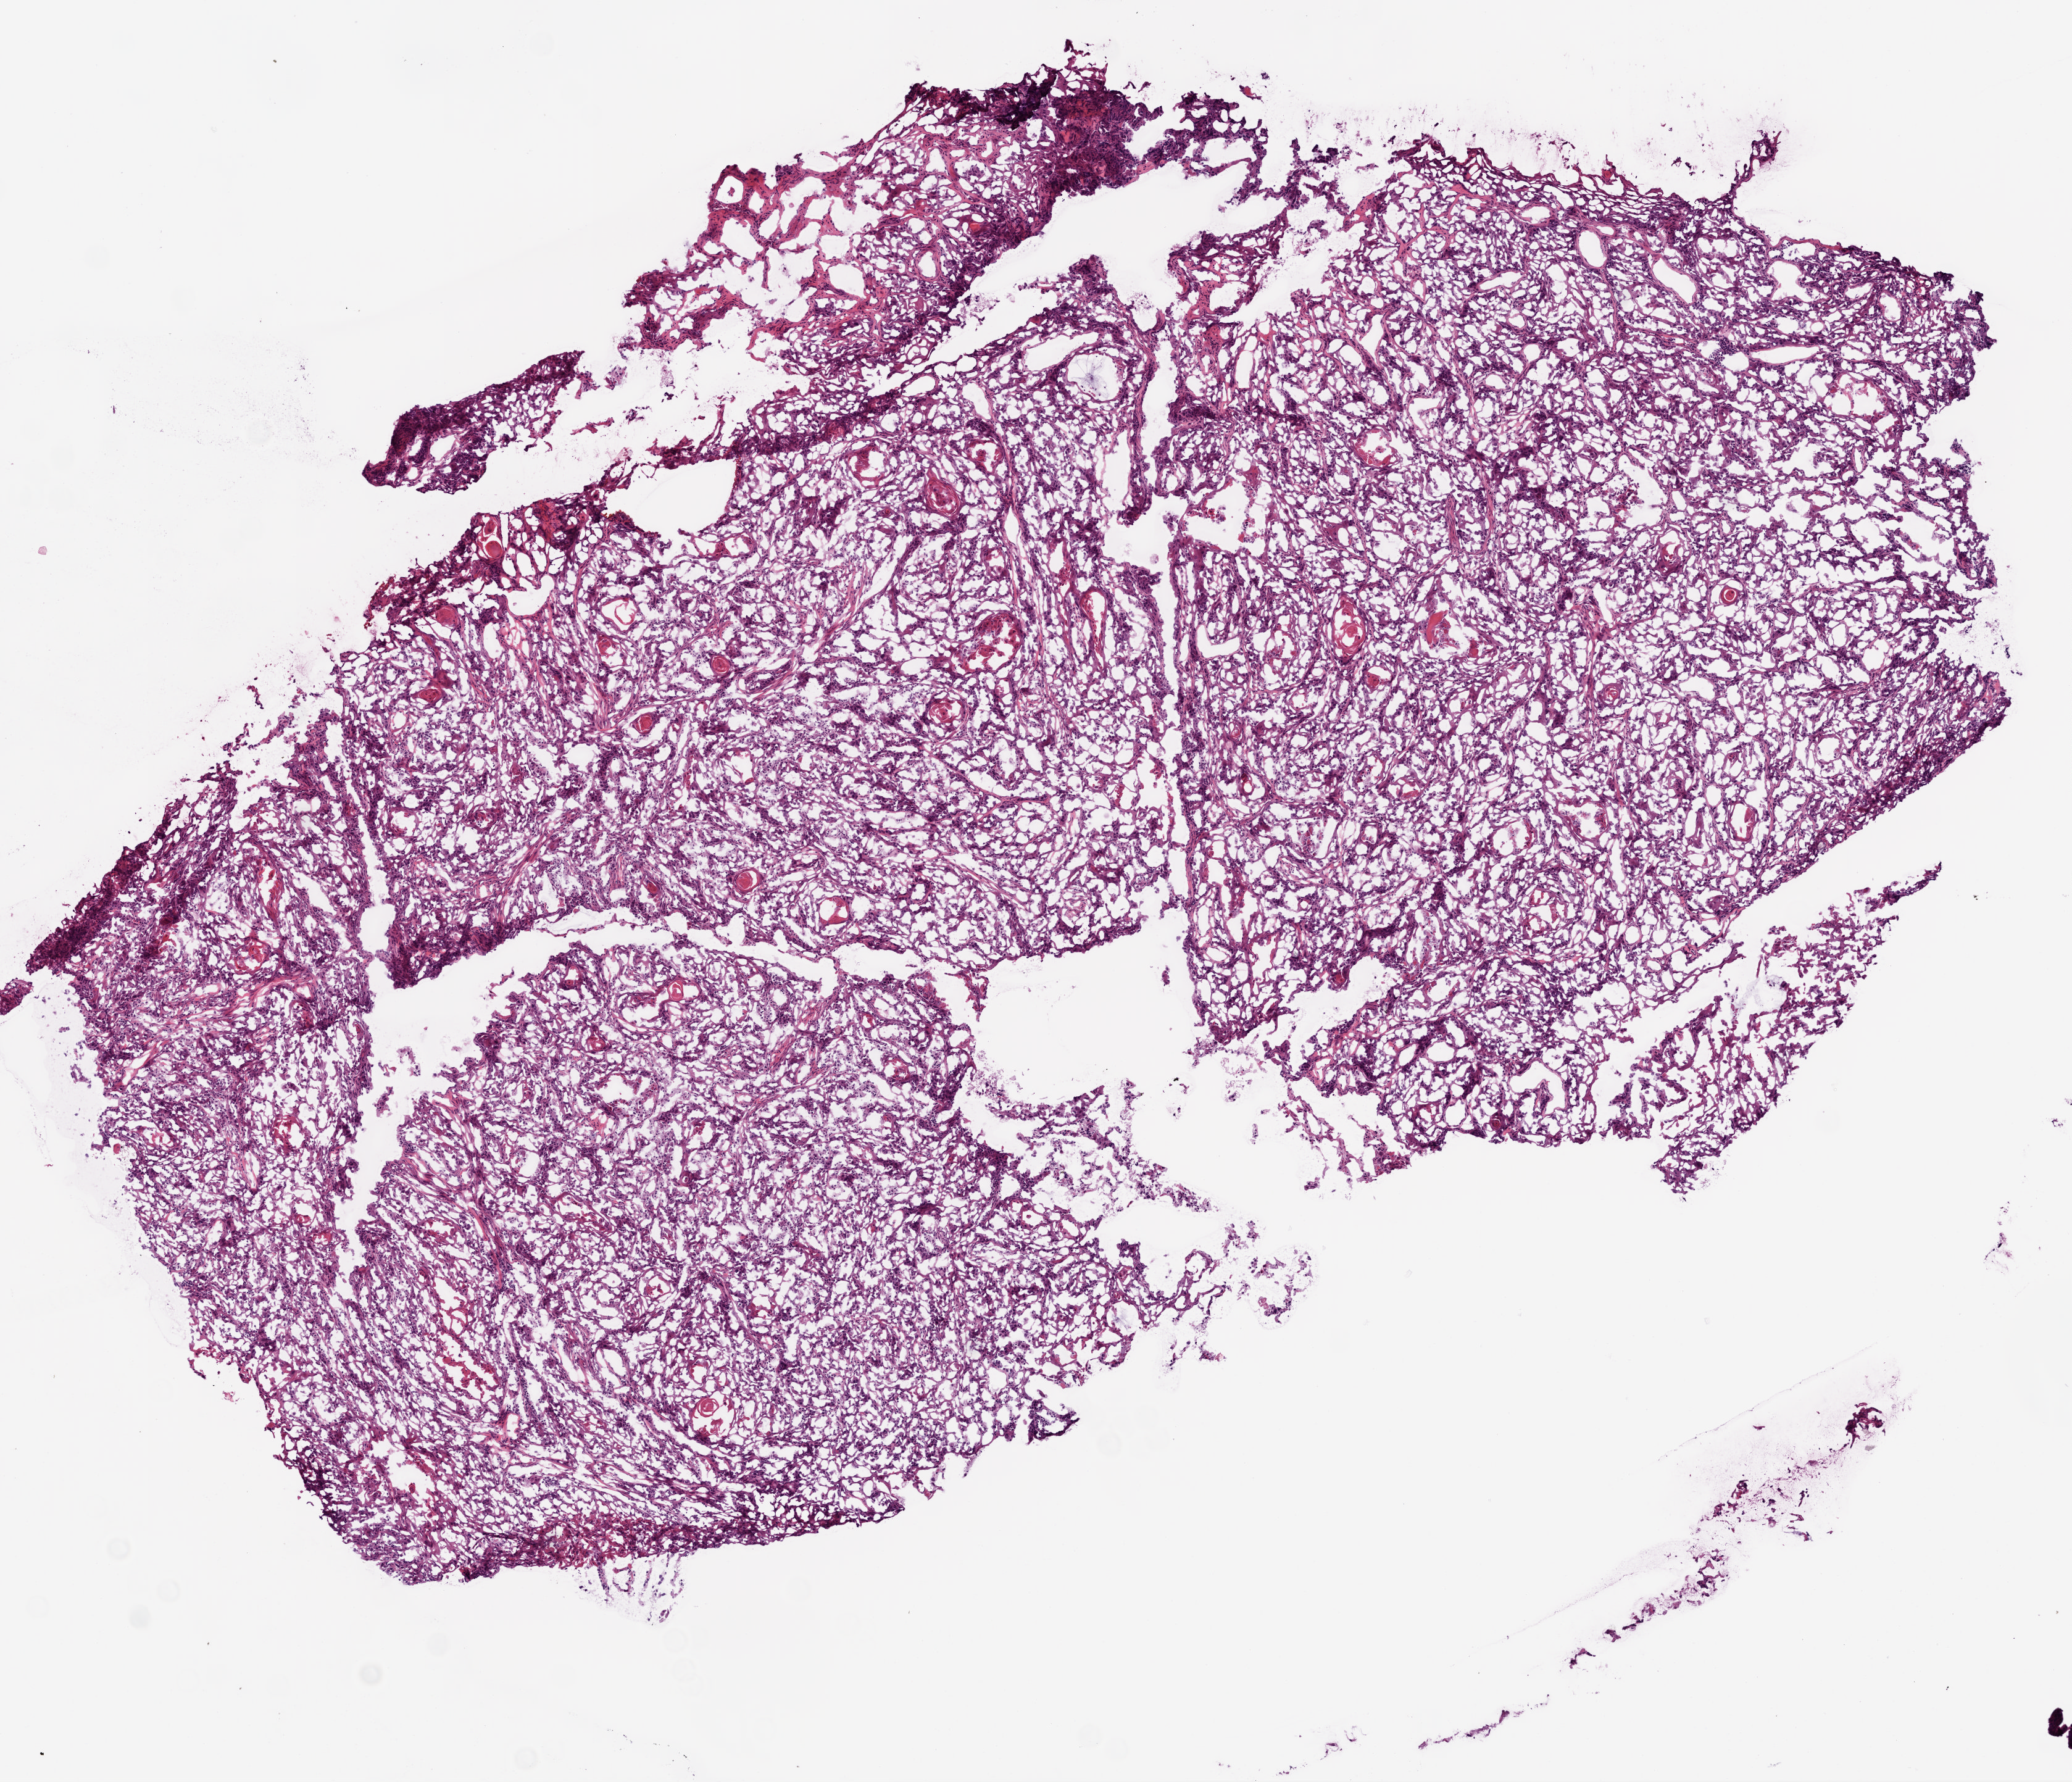
H&E whole-slide image, low-resolution overview of the scanned area, about 6.8 x 5.8 mm; frozen section; primary tumour sample from the head and neck. Male, age 43 years at initial diagnosis. Histologic grade: G3 (poorly differentiated). Composition of this section per pathologist review: tumour cells 90%, tumour nuclei 65%, normal cells 0%, stromal cells 10%, necrosis 0%.
Diagnosis: Squamous cell carcinoma, NOS (overlapping lesion of lip, oral cavity and pharynx). AJCC pathologic stage: IVB.